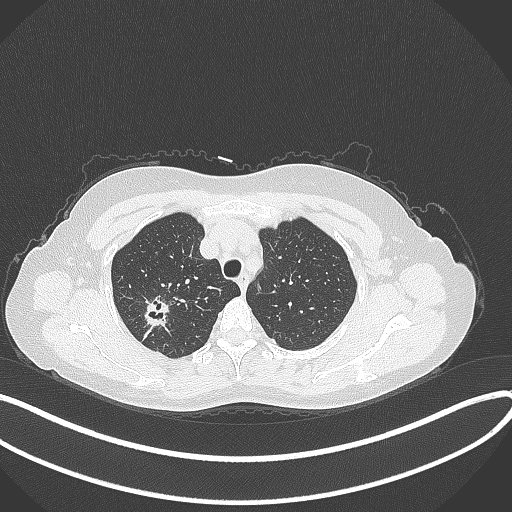
Chest CT, one axial slice; position 294 of 337 along the scan axis; reconstruction kernel B70f; 120 kVp; lung window (W 1500 / L -600 HU); 1 mm slice thickness; 512 × 512 image matrix, field of view 400 × 400 mm. Female patient, age 50 years. Case-level facts recorded for this patient, not image findings: clinical TNM (as recorded): T1c N0 M0.
Annotated regions visible in this slice (bounding box drawn by a radiologist):
- lung tumour (recorded histology: adenocarcinoma): bounding box <140,296,170,325> (left, top, right, bottom; pixels)